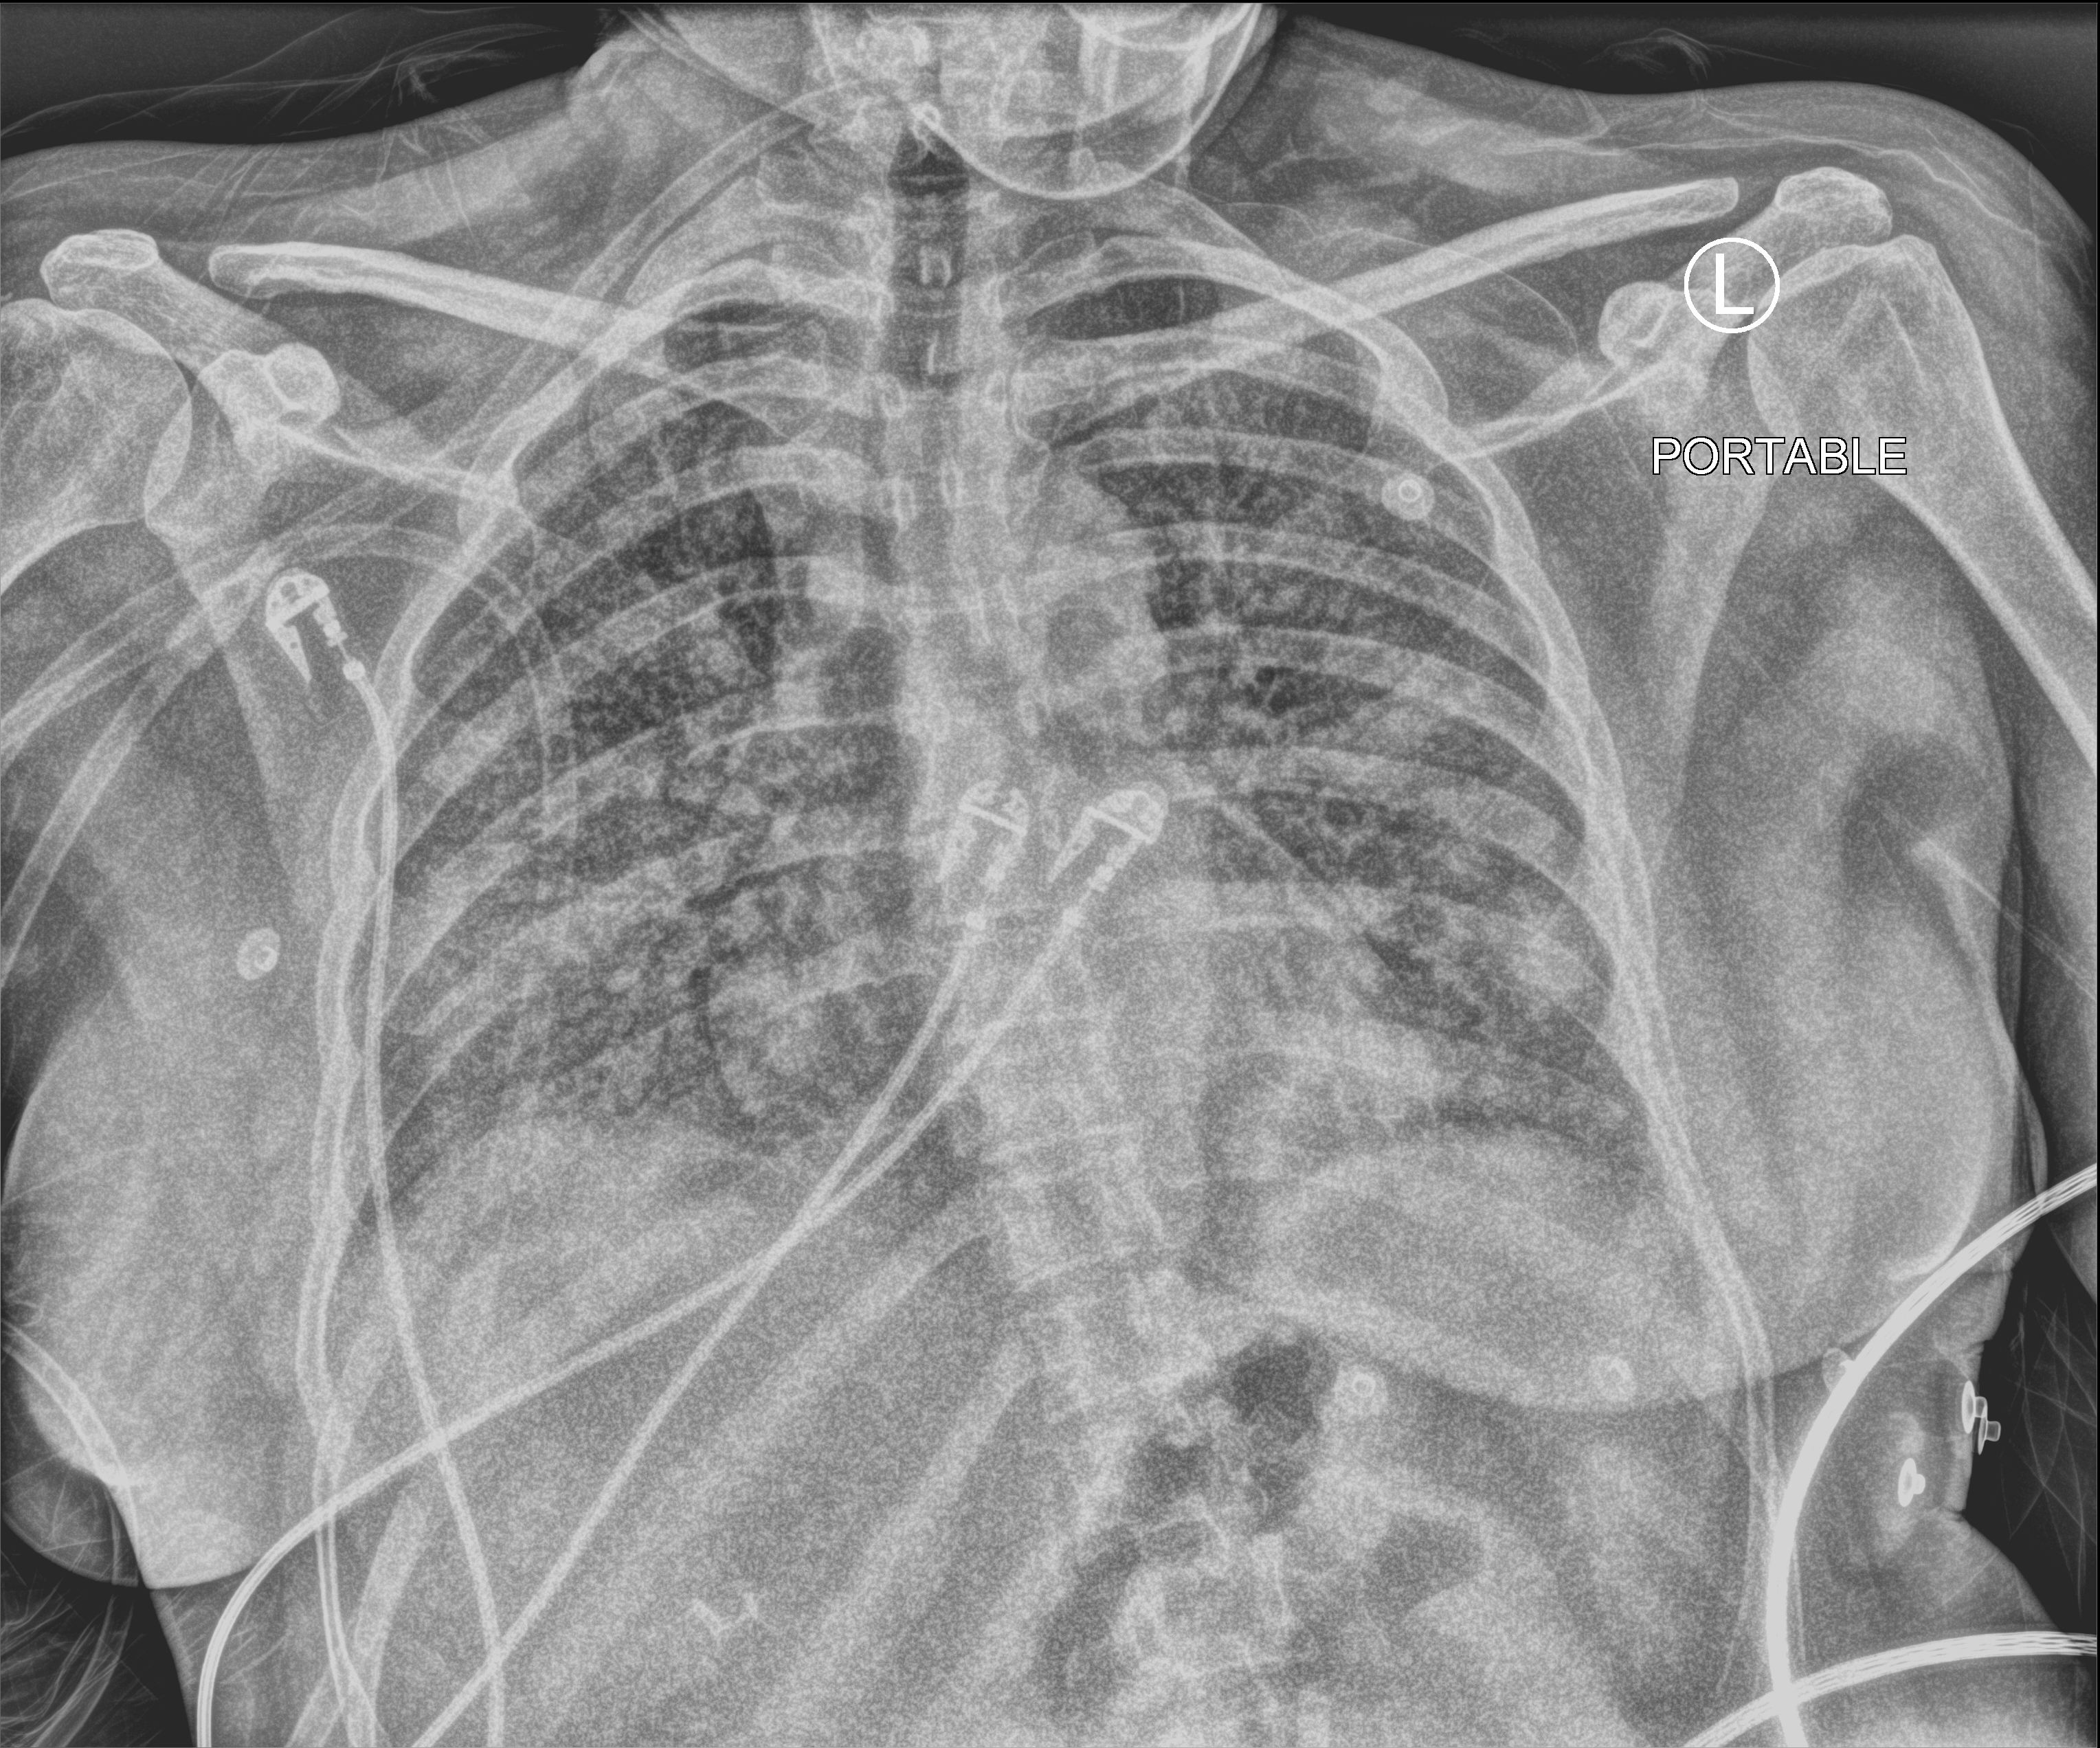
Chest X-ray (portable); anteroposterior (AP) projection. Patient hospitalised with COVID-19; female, aged 18–59 years.
Hospital-stay facts (about this admission, not read from this image; timing relative to this image not recorded): length of hospital stay: 25 days; mechanically ventilated during this hospital stay: no.